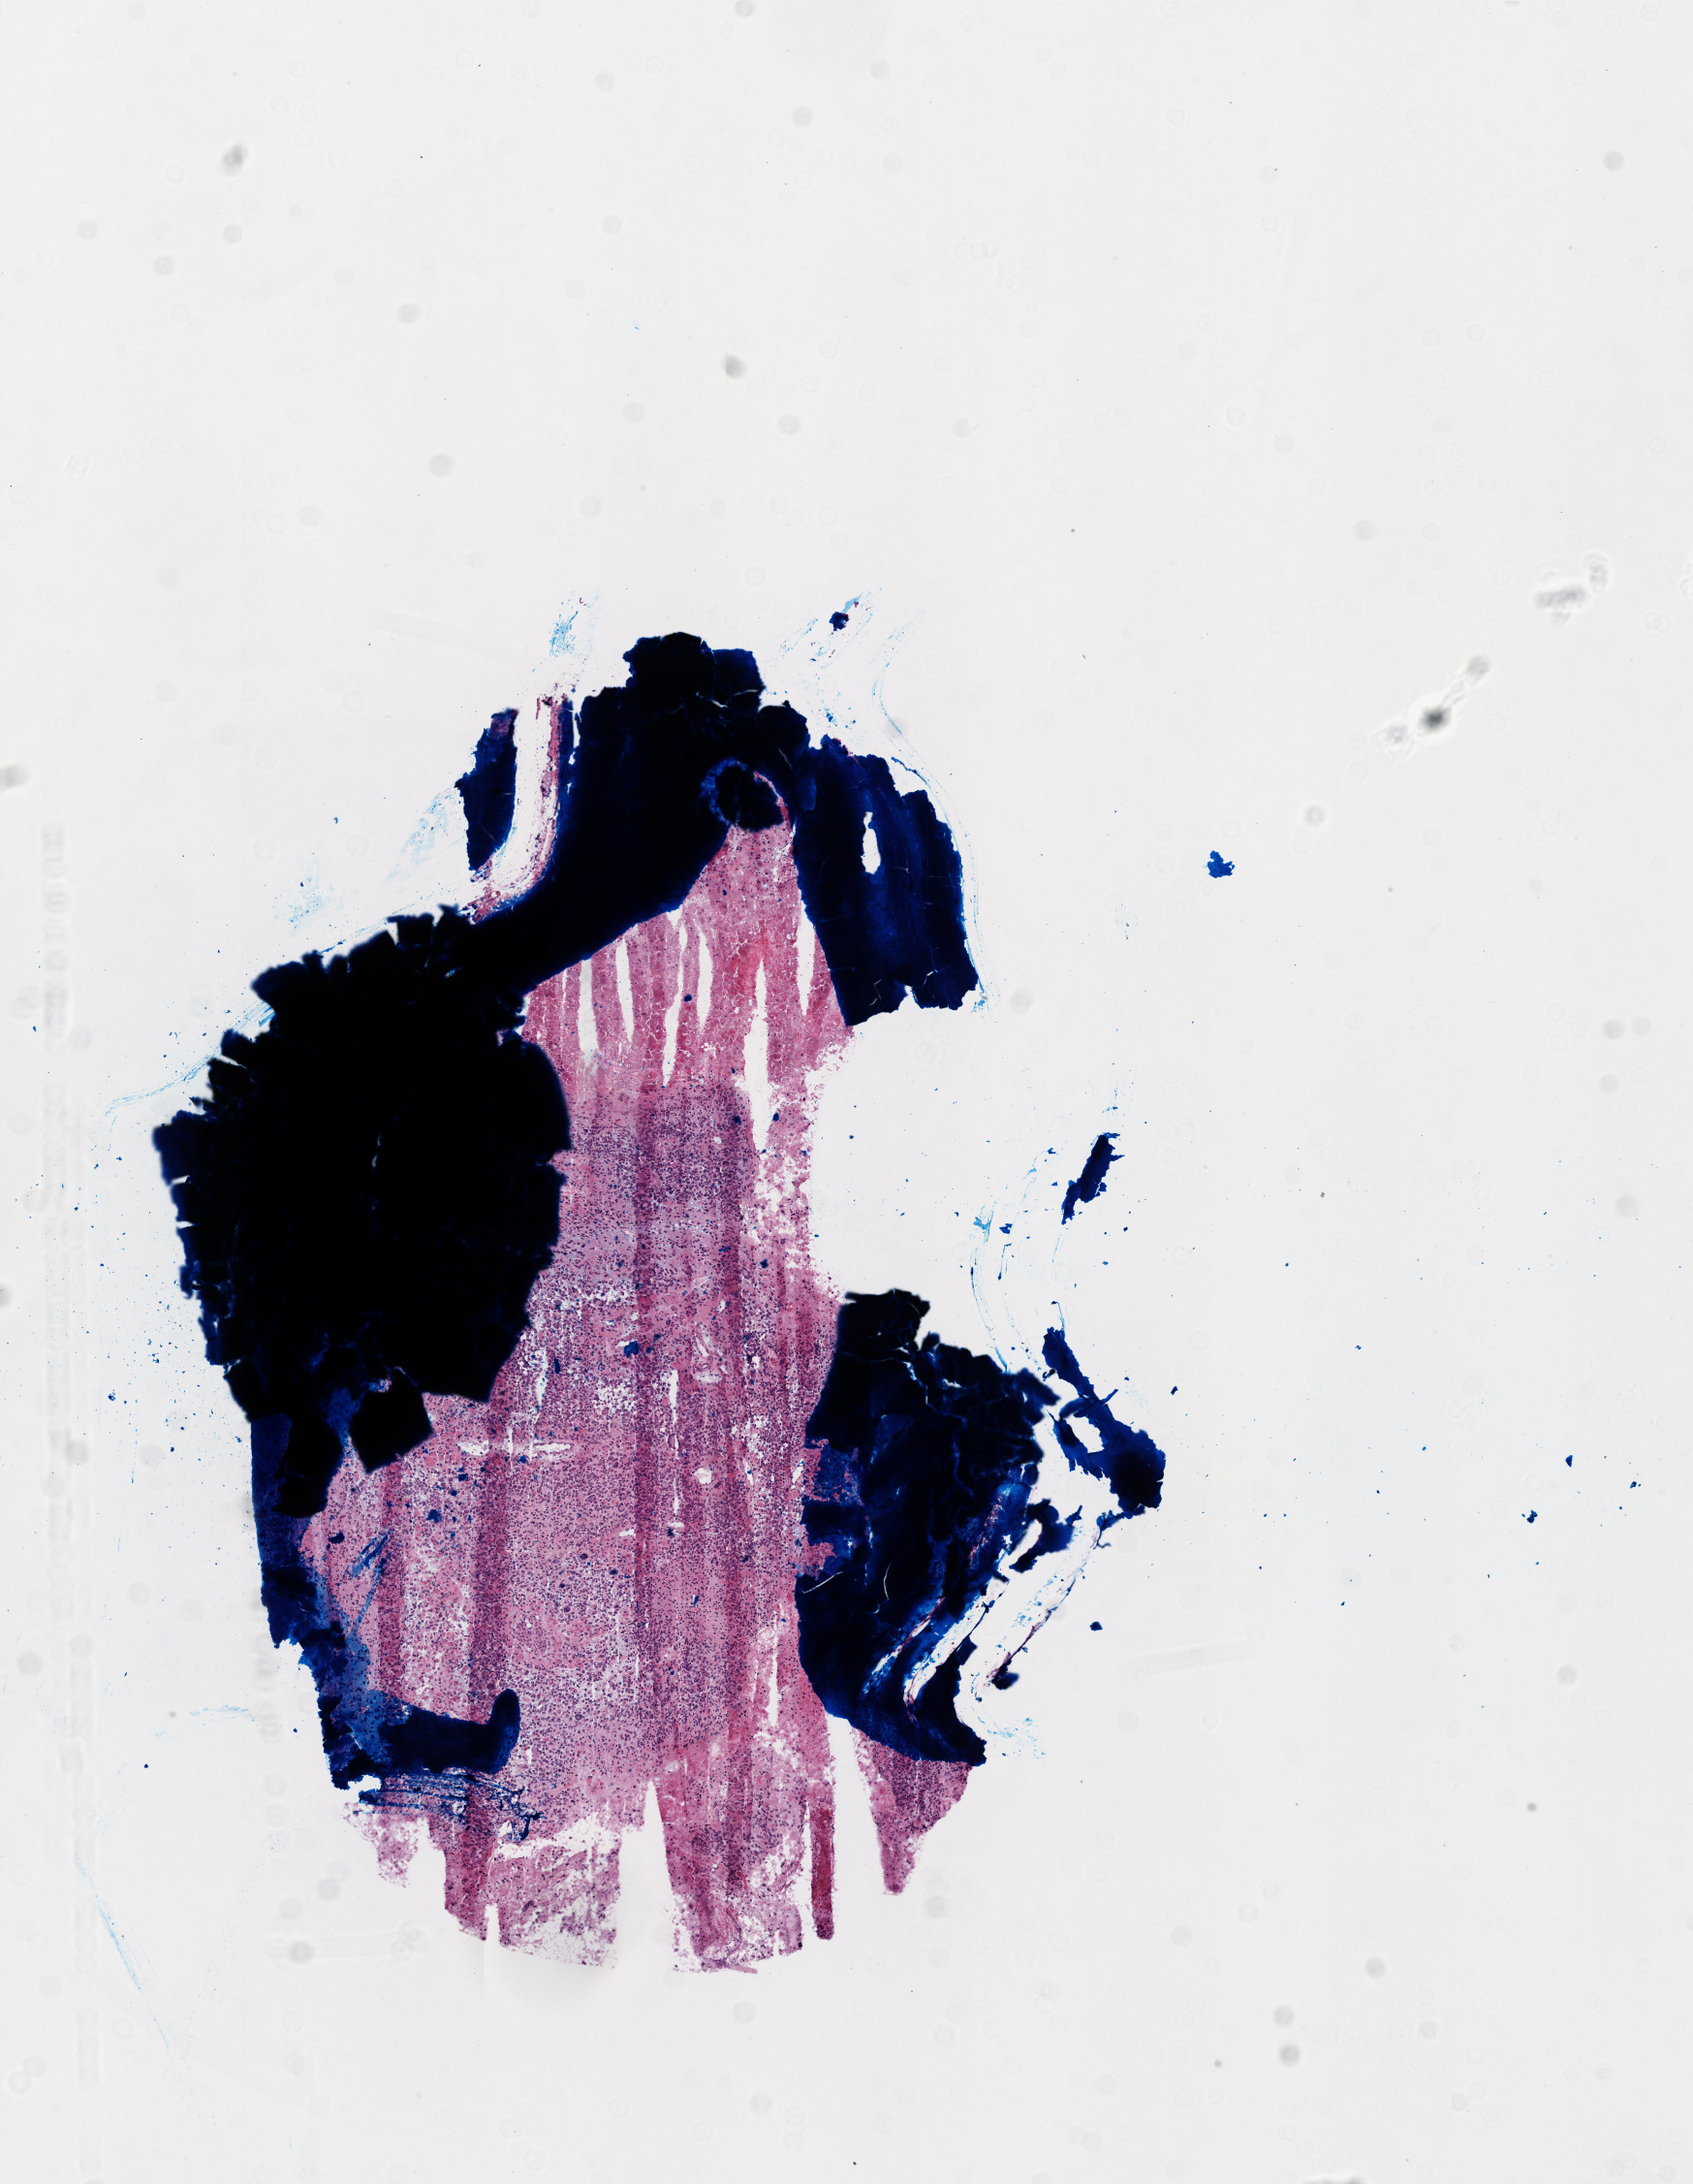
Whole-slide histology image, H&E — low-resolution overview of the scanned area, about 7.0 x 9.0 mm; frozen section from the top of the tissue portion; sample: primary tumour, brain. Patient: female, age at initial diagnosis 72 years. Composition of this section per pathologist review: tumour cells 75%, tumour nuclei 100%, normal cells 0%, stromal cells 0%, necrosis 25%.
* pathologic diagnosis: Glioblastoma